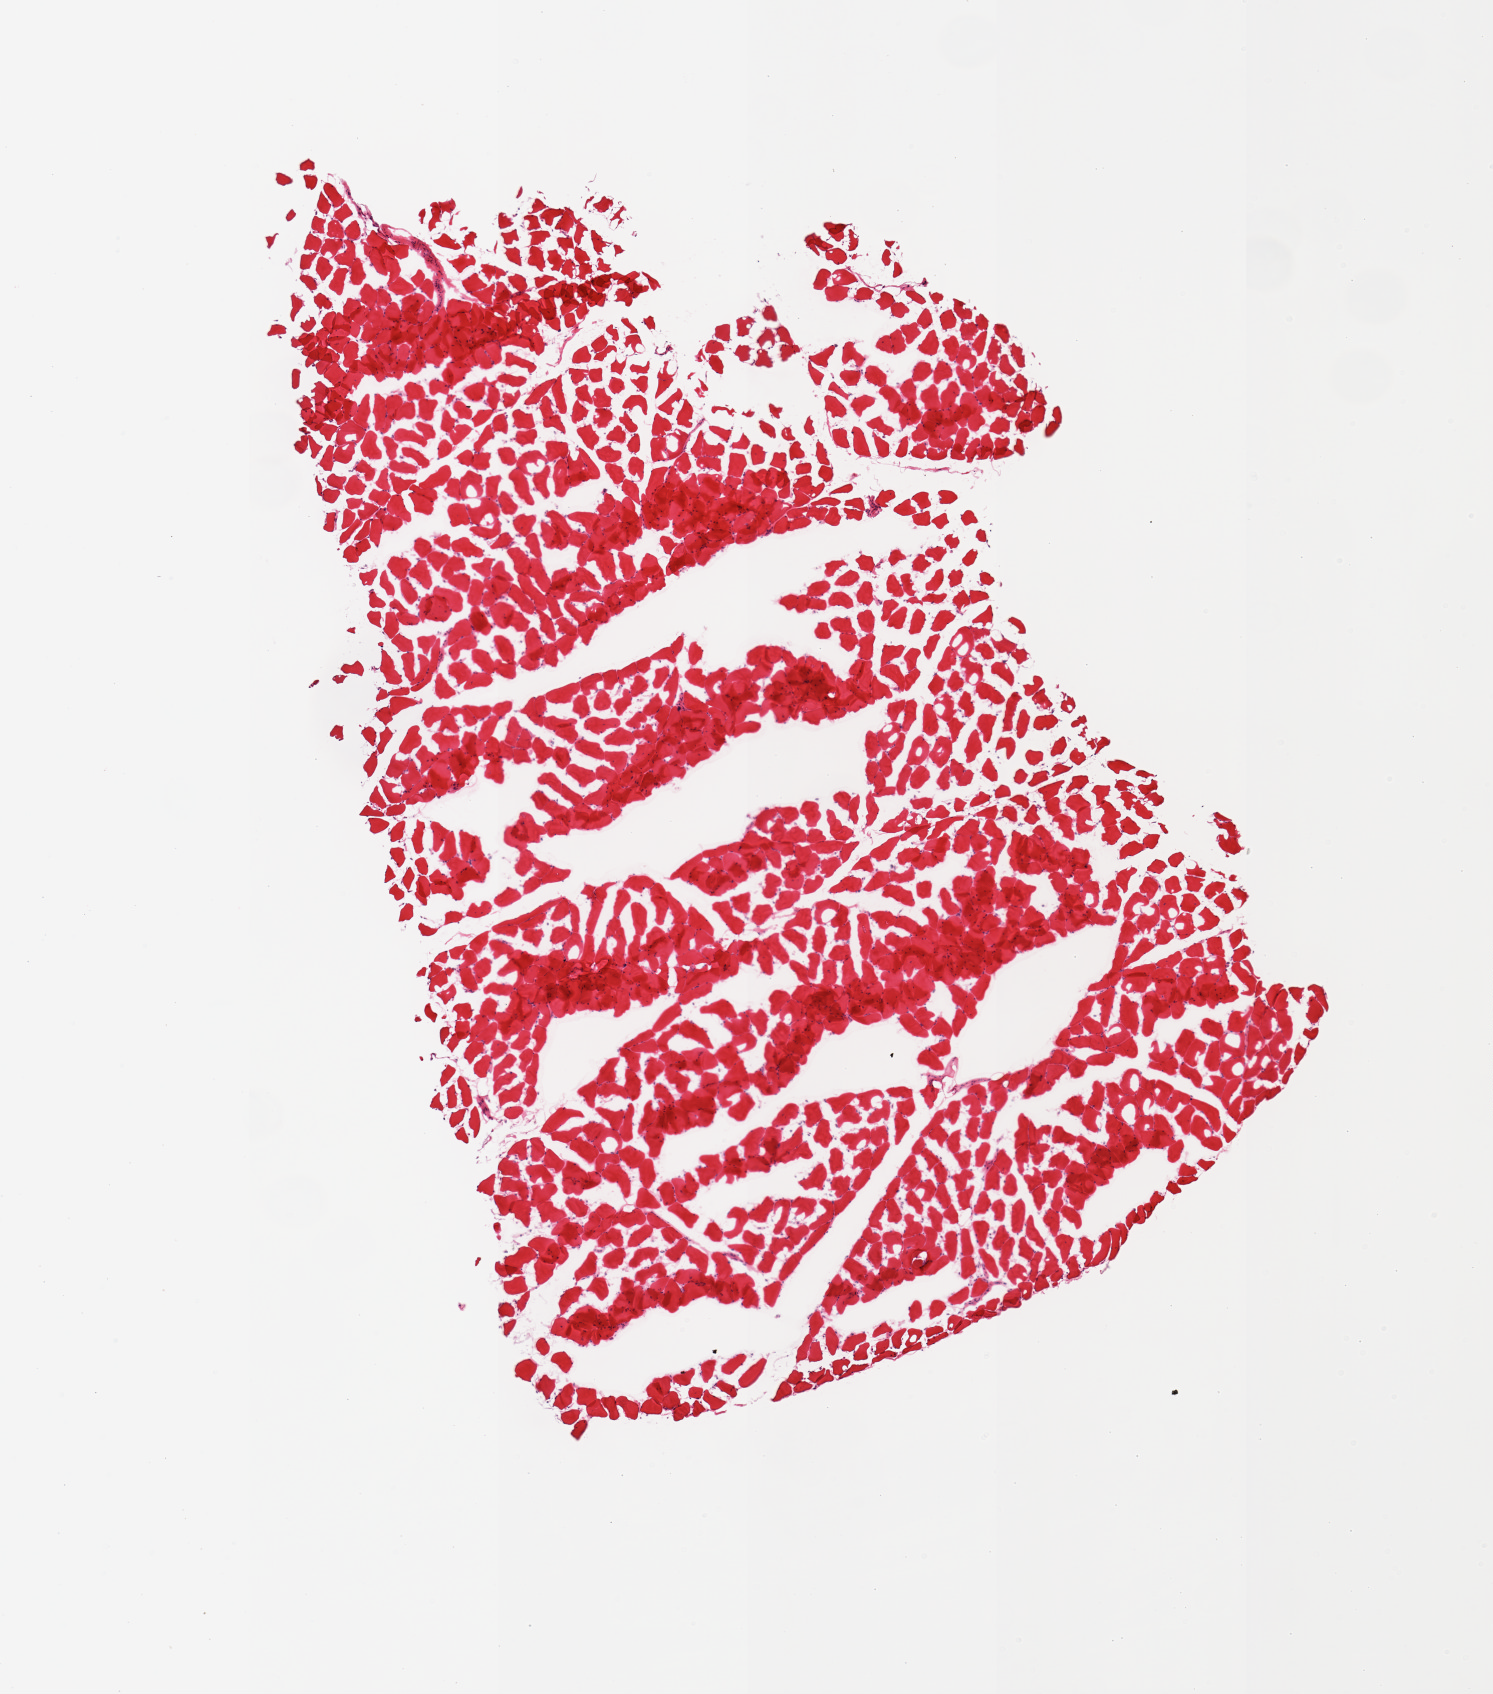
Digitized haematoxylin and eosin-stained section, low-resolution overview of the scanned area, about 5.9 x 6.7 mm (slide scanned at 20x), frozen section, section of skeletal muscle (target tissue), donor tissue sample. Donor: female.
- reviewer comment on this tissue sample: 1 piece